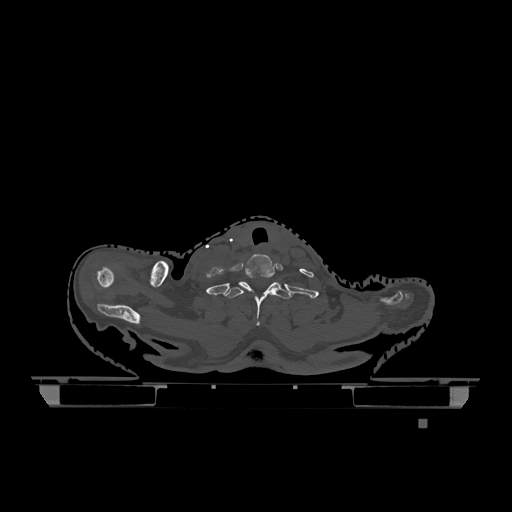
CT including the spine, one axial slice. Position 1011 of 1317 along the scan axis. Bone window (W 1800 / L 400 HU). 512 × 512 image matrix, field of view 500 × 500 mm. Patient: female, 74 years. Case-level facts recorded for this patient, not image findings: primary cancer: lung; vertebrae with lytic lesions (as recorded): T1, T4, T5, T6, L4, L5.
Outlined on this slice (semi-automatically segmented with operator editing):
- T1 vertebra: box from (x=223, y=281) to (x=292, y=326) px